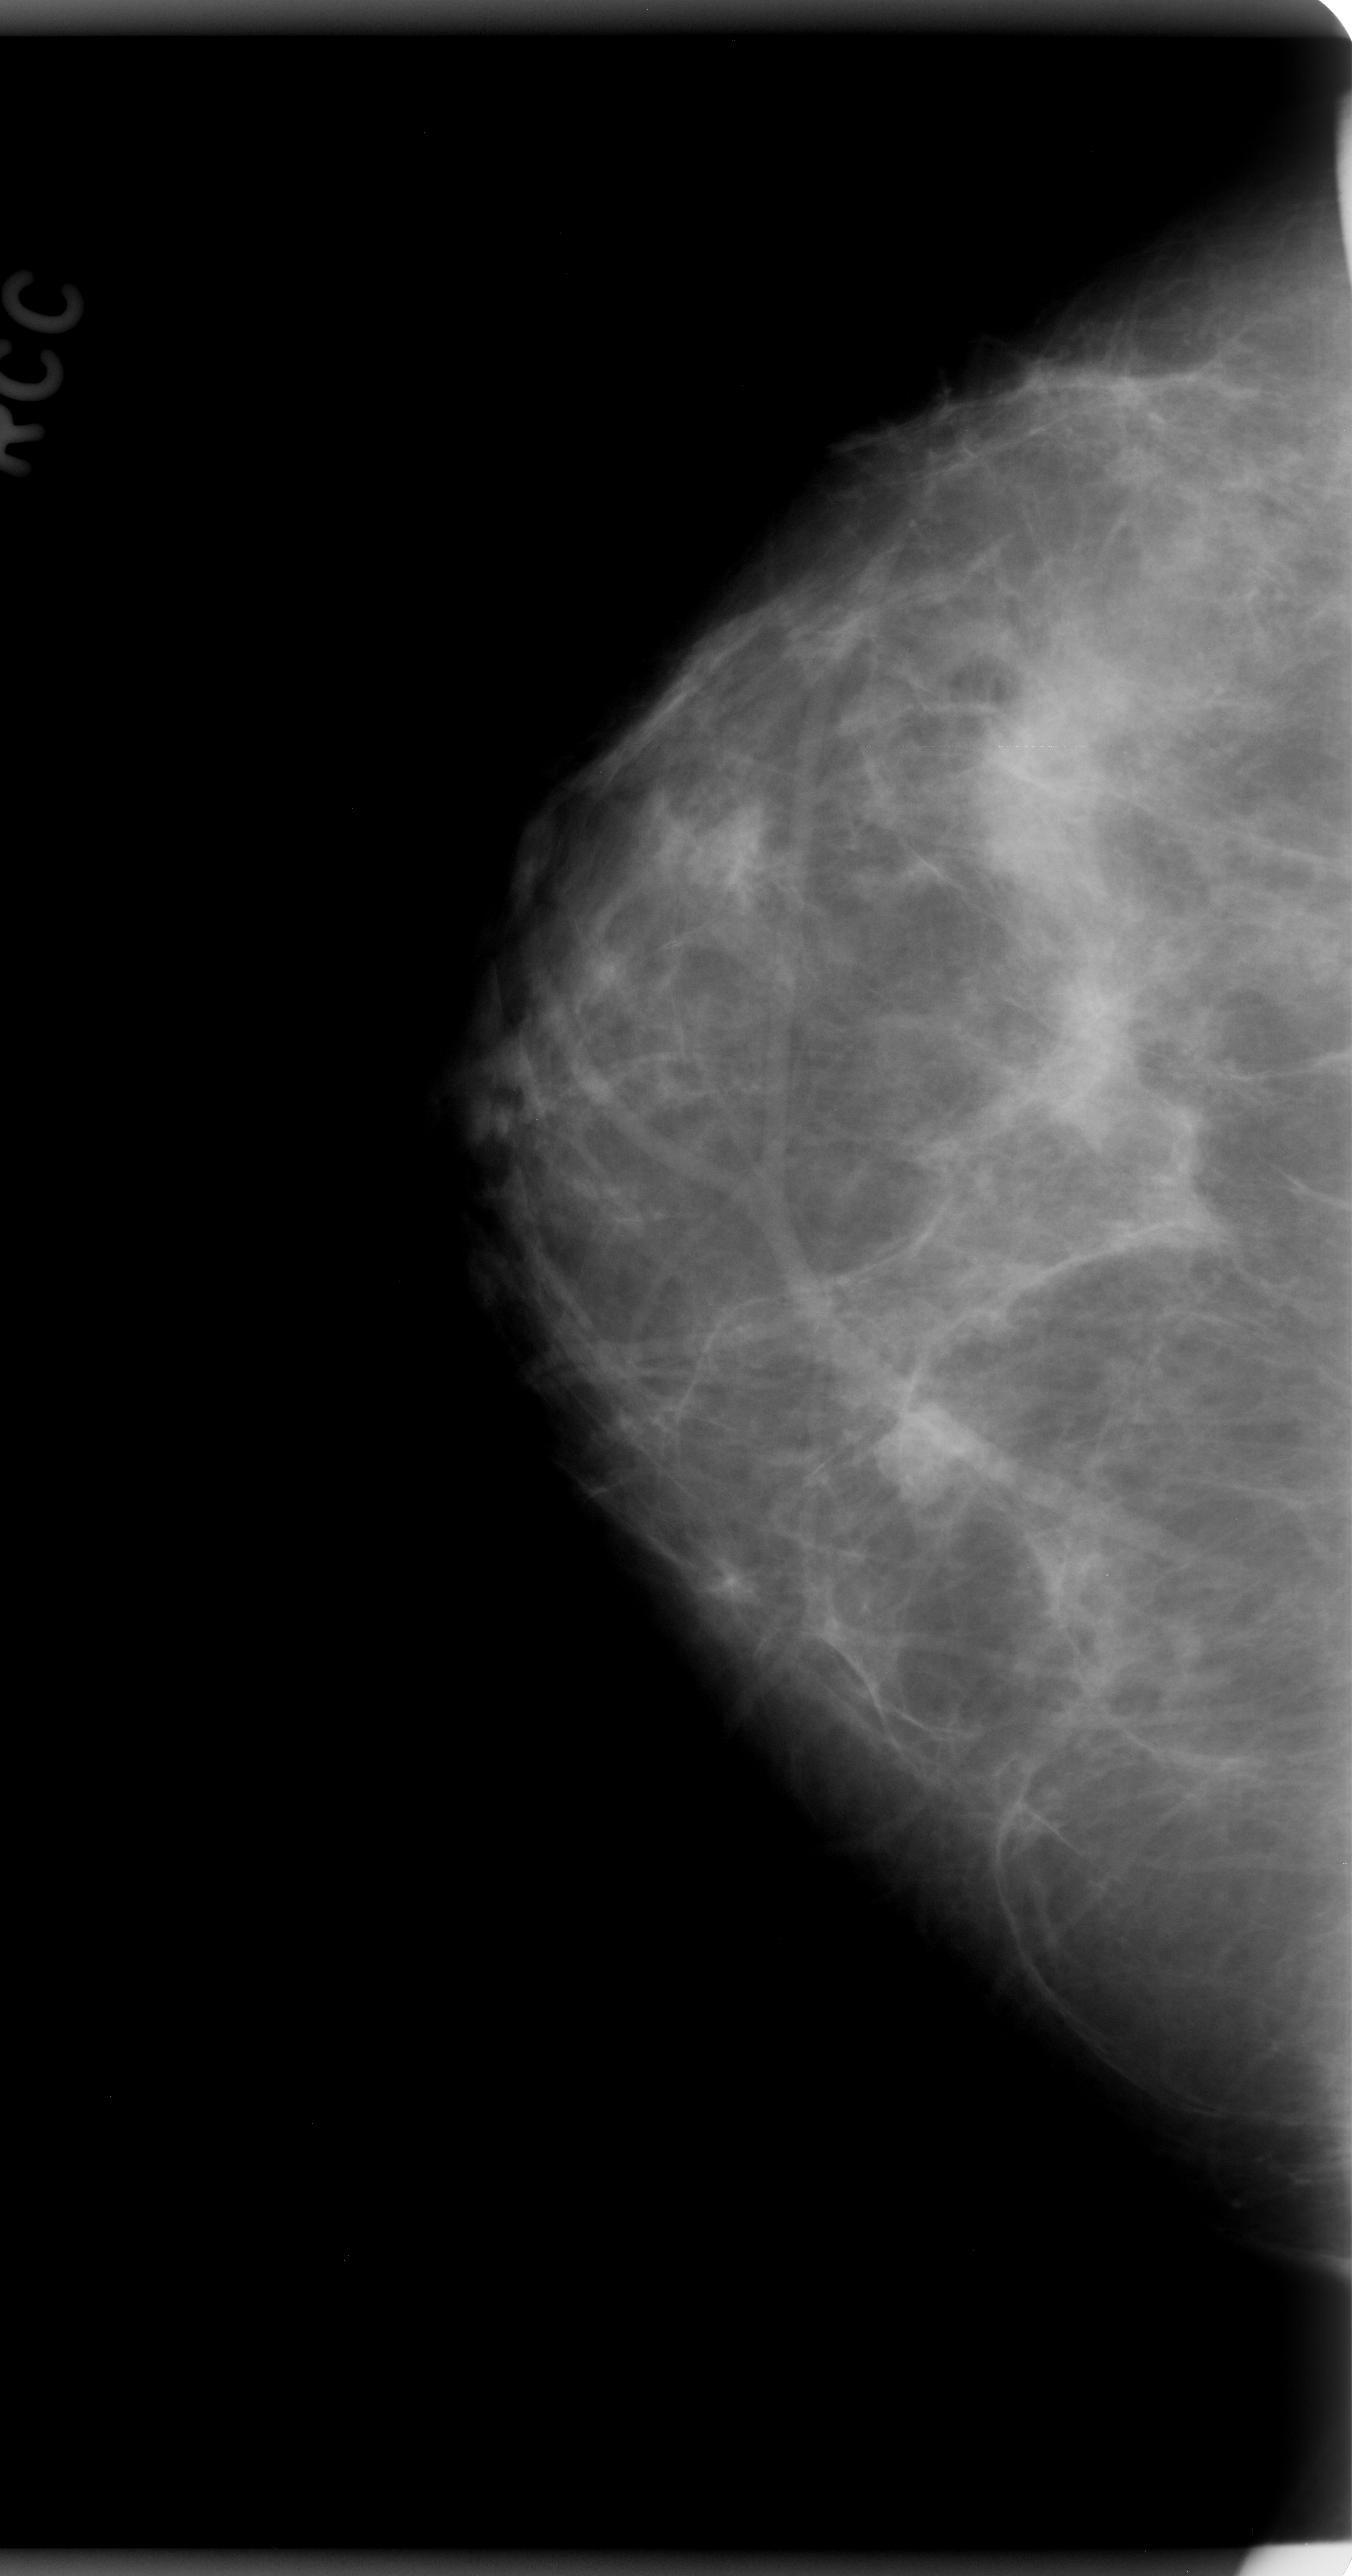
Scanned film-screen mammogram; right breast; craniocaudal (CC) view; breast composition: scattered fibroglandular densities (BI-RADS density category 2 of 4); 1352 × 2576 image matrix.
Expert-marked regions of interest on this film, with their recorded descriptors:
- mass, shape oval, margins microlobulated; BI-RADS assessment category 4; pathology (as recorded): benign: bounding box <854,1376,1013,1519> (left, top, right, bottom; pixels)